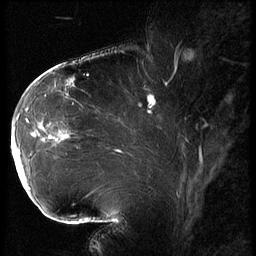
Breast MRI (dynamic contrast-enhanced), one sagittal slice; position 40 of 62 along the scan axis; 3 images stored at this slice position (order not interpretable as contrast timing); 1.5 T; TE 4.2 ms, TR 9 ms; 2.5 mm slice thickness; 256 × 256 image matrix. Female patient, age 43 years. Case-level facts recorded for this patient, not image findings: setting: breast cancer imaged before/during neoadjuvant chemotherapy; receptor status: HER2-positive.
Structures marked on this image (semi-automatically segmented with operator editing):
- analysis volume of interest (the breast-tissue region the enhancement analysis was run in; not a lesion): bounding box [x1, y1, x2, y2] px = [11, 90, 82, 203]
- tumour enhancement mask (voxels above the 140 % enhancement threshold inside the analysis volume of interest): [12, 123, 70, 190]